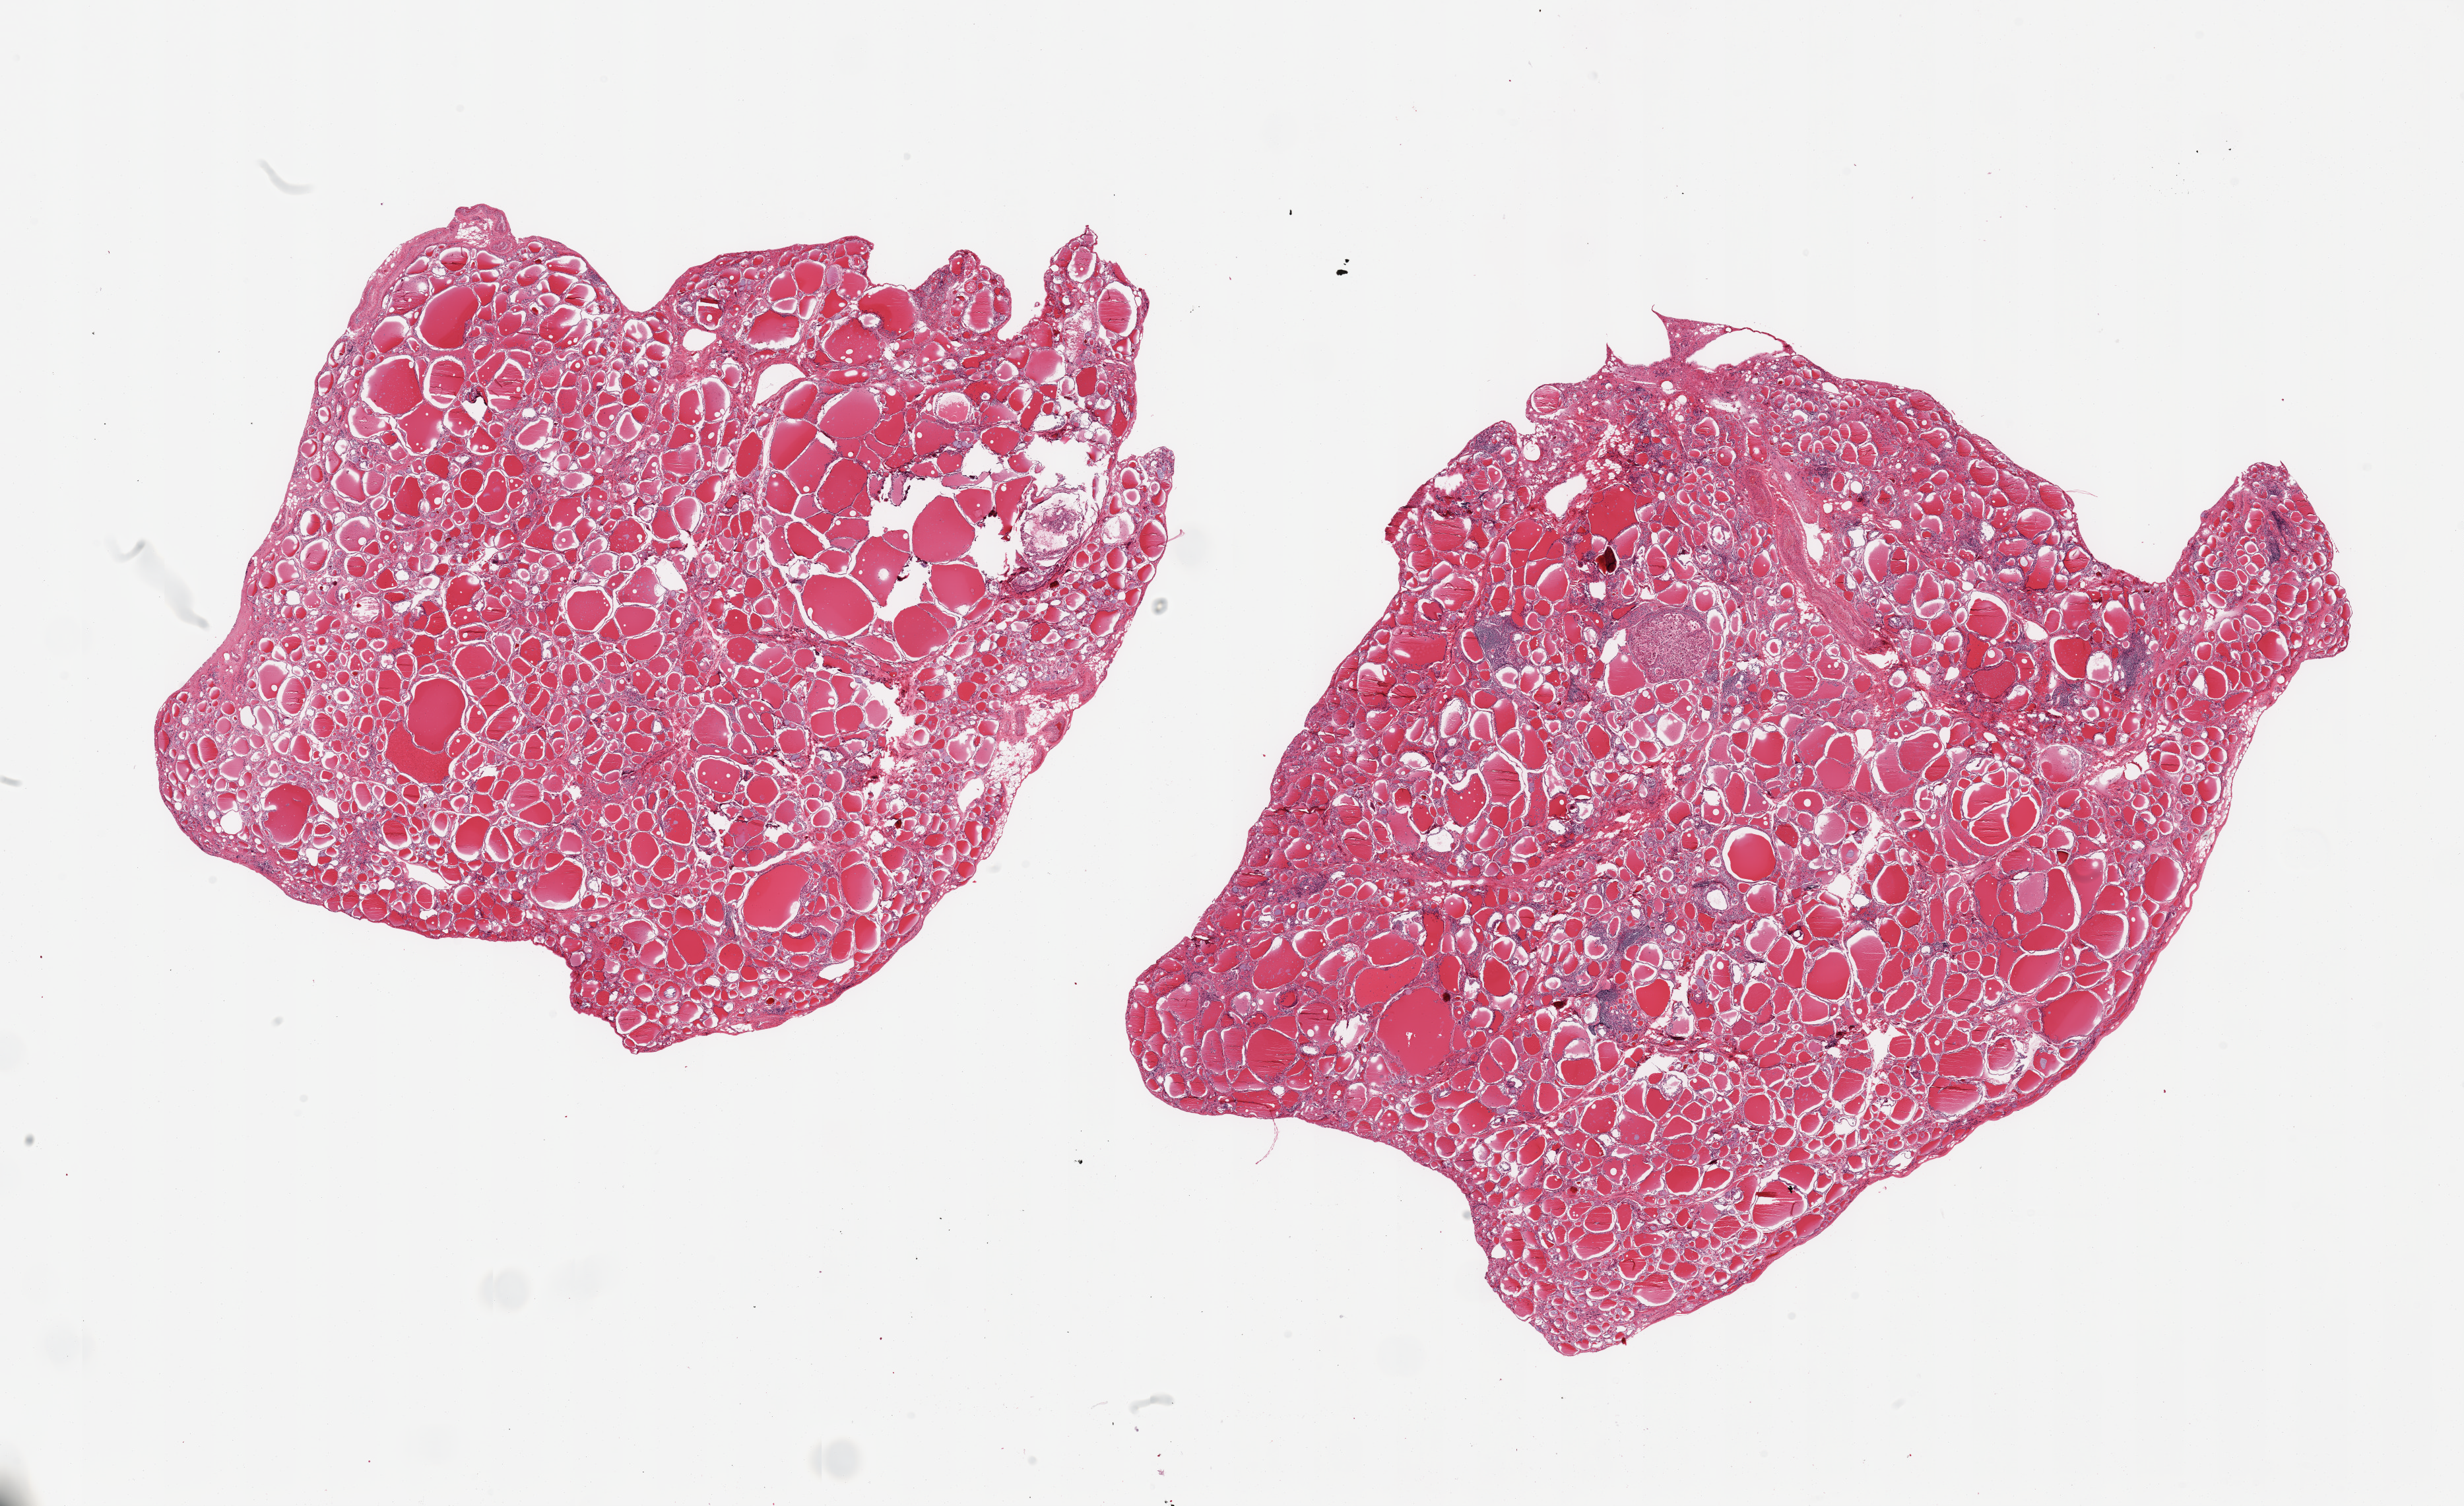
H&E whole-slide image — a low-resolution overview of the entire scanned area, about 29.5 x 18.0 mm; PAXgene-fixed paraffin-embedded (PFPE) section; section of thyroid (target tissue); donor tissue sample.
Reviewer comment on this tissue sample: 2 pieces; mild lymphocytic thyroiditis with 1mm Hurthle cell lesion.